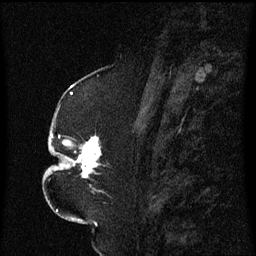
Breast MRI (dynamic contrast-enhanced), one sagittal slice; position 29 of 60 along the scan axis; dynamic contrast-enhanced series, image 2 of 3 at this slice position (ordered by acquisition); 1.5 T; TE 4.2 ms, TR 8.4 ms; 2.3 mm slice thickness; 256 × 256 image matrix. Patient: female, 52 years. From the clinical record (not read from this slice): setting: breast cancer imaged before/during neoadjuvant chemotherapy; receptor status: HR-positive, HER2-negative.
Structures marked on this image (semi-automatic segmentation, software-assisted and operator-edited):
- analysis volume of interest (the breast-tissue region the enhancement analysis was run in; not a lesion): bounding box (x1, y1, x2, y2) in pixels: (49, 124, 109, 193)
- tumour enhancement mask (voxels above the 70 % enhancement threshold inside the analysis volume of interest): (55, 136, 101, 179)